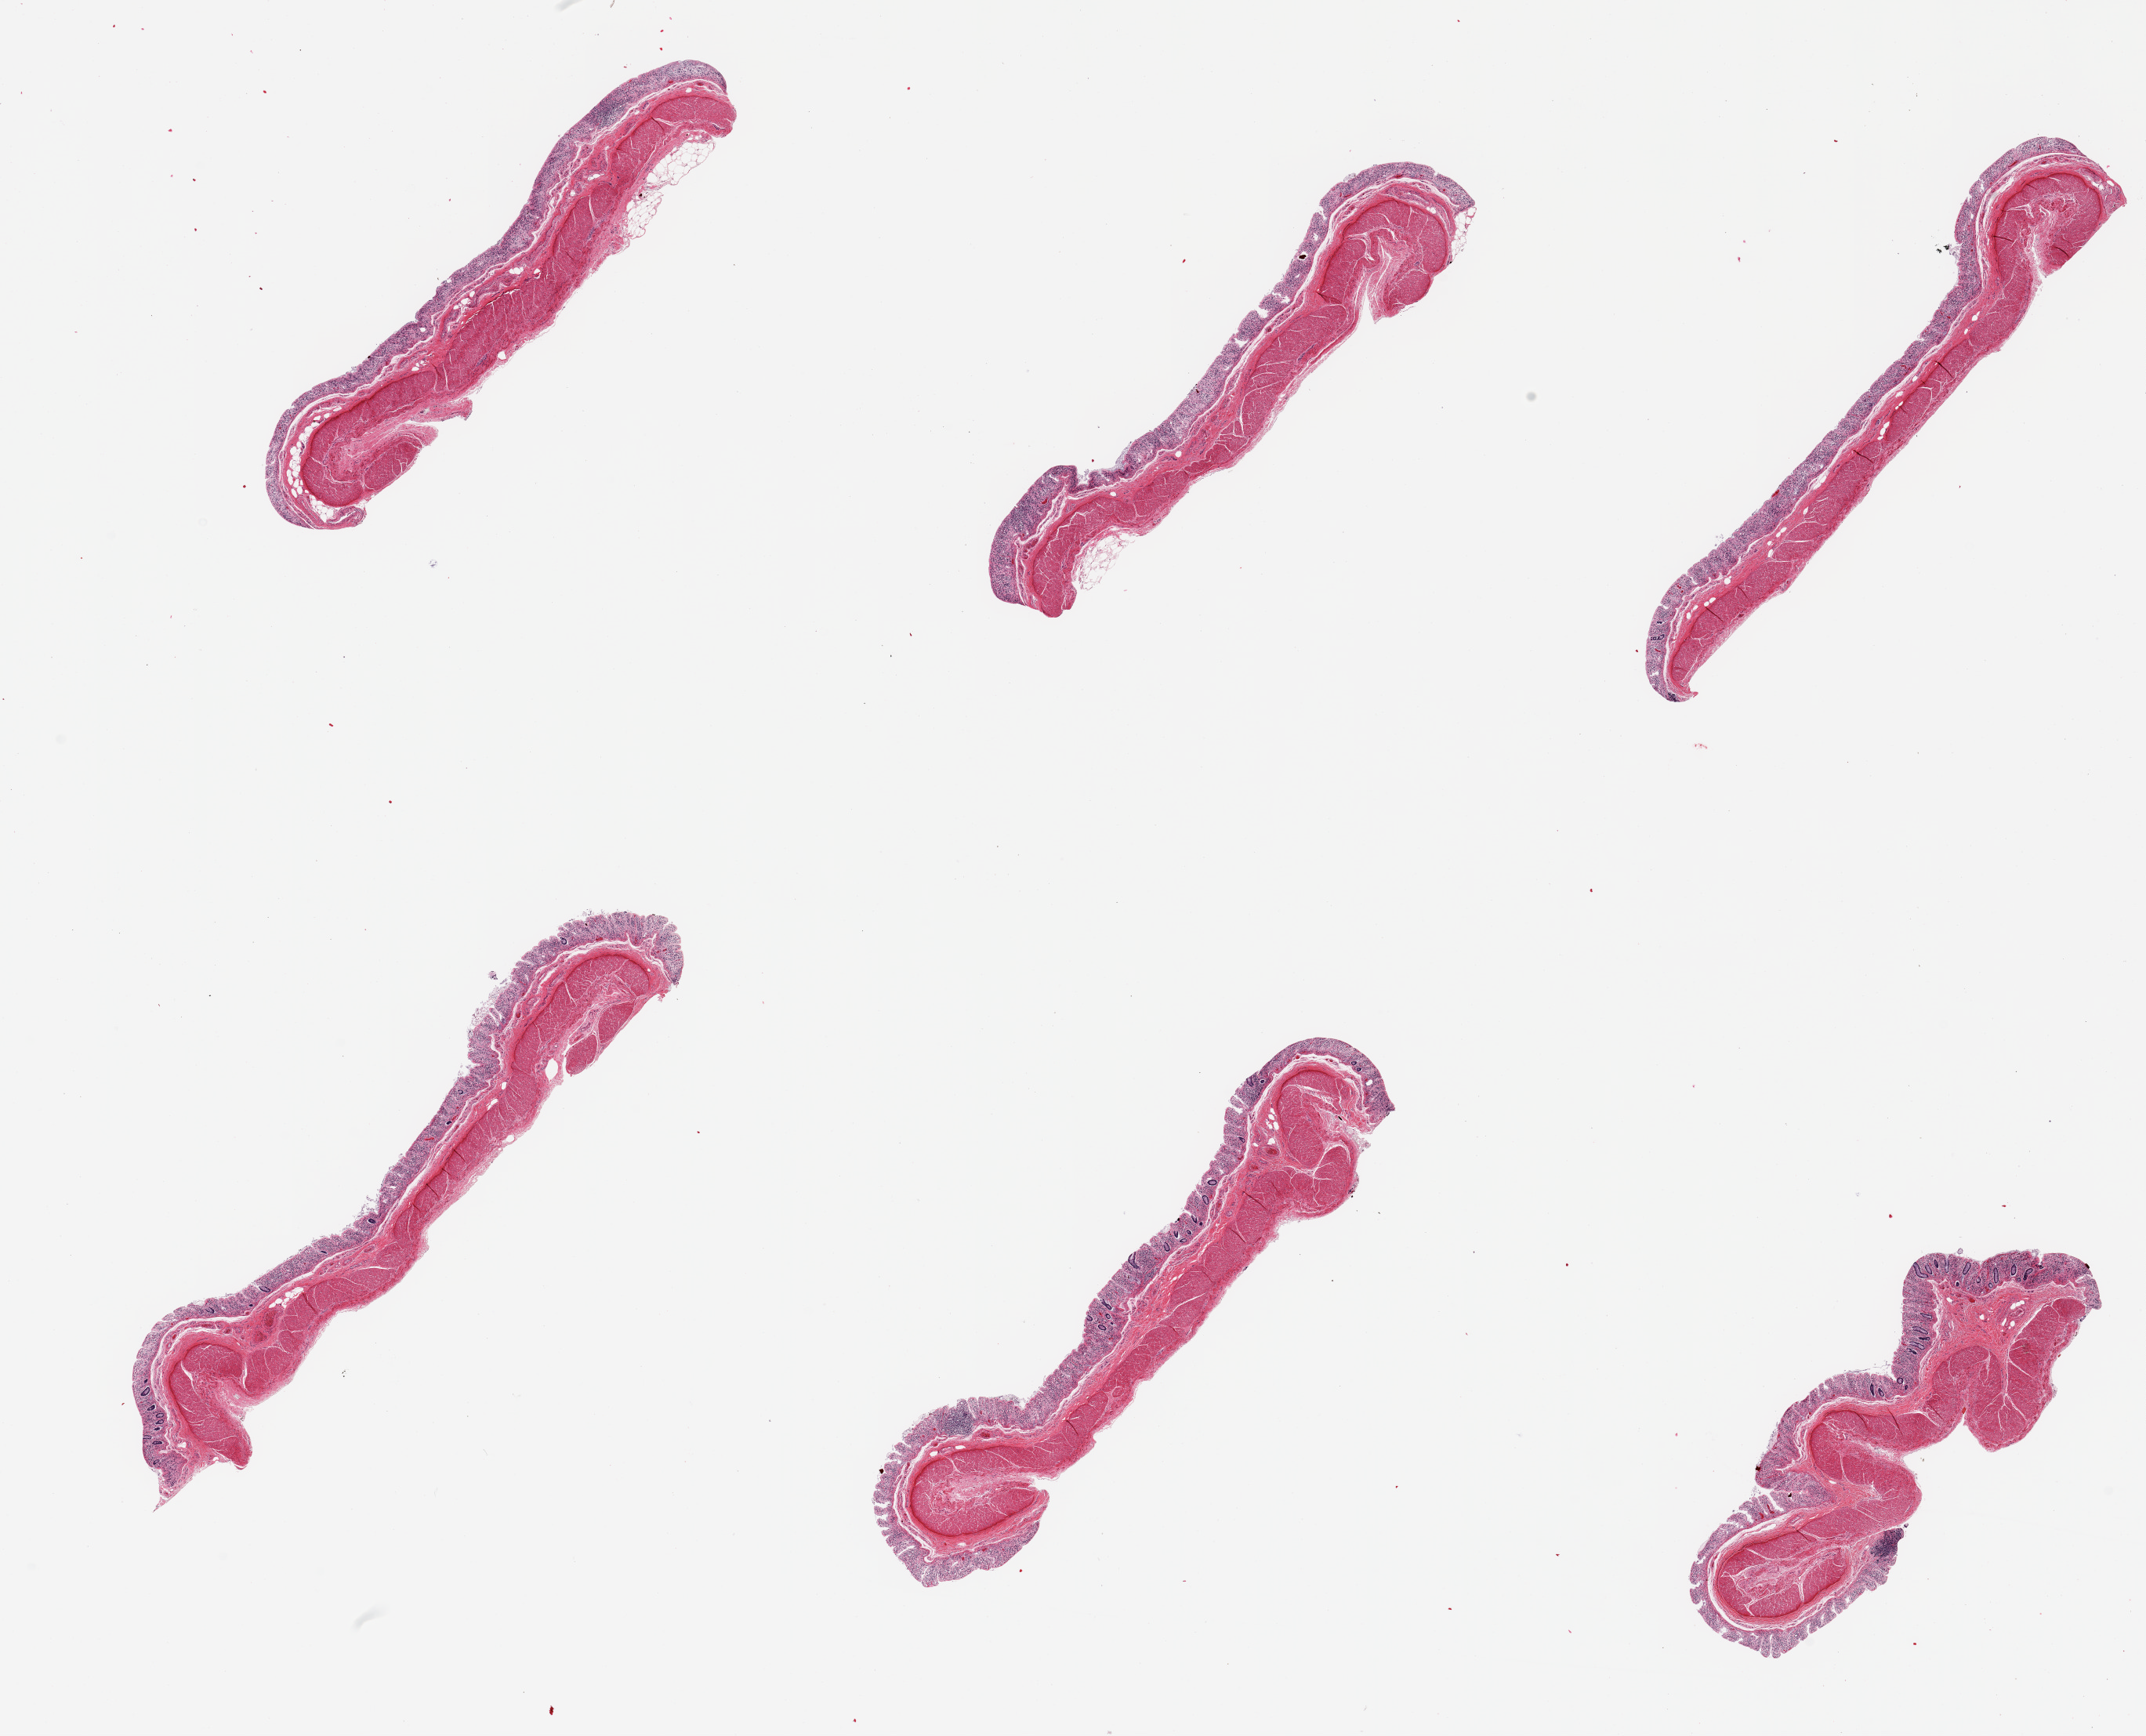
H&E whole-slide image, brightfield, low-resolution overview of the scanned area, about 21.7 x 17.5 mm, PAXgene-fixed paraffin-embedded (PFPE) section, target tissue: transverse colon, tissue donor sample. Donor sex: female.
Pathologist's review note for this sample: 6 pieces; mucosa autolyzed; muscularis intact [1].